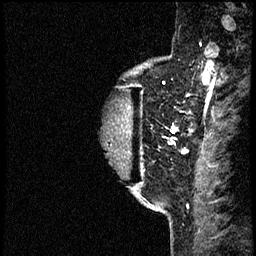
Breast MRI (dynamic contrast-enhanced), one sagittal slice. Slice 50 of 60 in the series (ordered by position). Dynamic contrast-enhanced study with each time point stored as its own series, time point 2 of 4 at this slice position (early post-contrast, ordered by acquisition time). 1.5 T. TE 4.2 ms, TR 17.6 ms. 256 × 256 image matrix. Female patient, age 40 years. From the clinical record (not read from this slice): setting: breast cancer imaged before/during neoadjuvant chemotherapy; receptor status: HER2-positive.
Structures marked on this image (semi-automatically segmented with operator editing):
- analysis volume of interest (the breast-tissue region the enhancement analysis was run in; not a lesion): bounding box (x1, y1, x2, y2) in pixels: (102, 56, 197, 205)
- tumour enhancement mask (voxels above the 100 % enhancement threshold inside the analysis volume of interest): (106, 101, 189, 153)